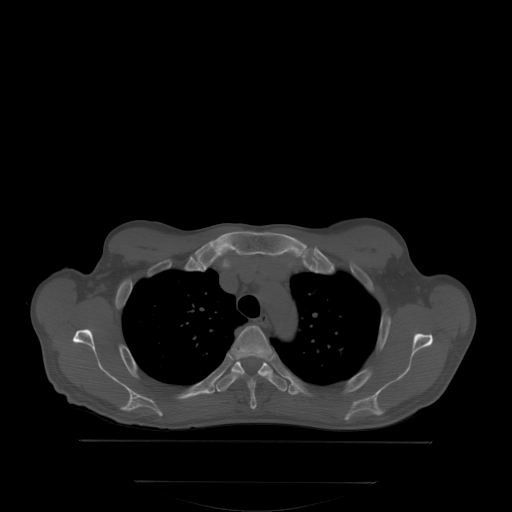
CT including the spine, one axial slice; slice 263 of 350 in the series (ordered by position); bone window (W 1800 / L 400 HU); 512 × 512 image matrix, field of view 500 × 500 mm. Male patient, age 58 years. From the clinical record (not read from this slice): primary cancer: prostate; vertebrae with lytic lesions (as recorded): L1.
Outlined on this slice (semi-automatically segmented with operator editing):
- T3 vertebra: bounding box [x1, y1, x2, y2] px = [233, 325, 273, 408]
- T4 vertebra: [214, 353, 289, 391]